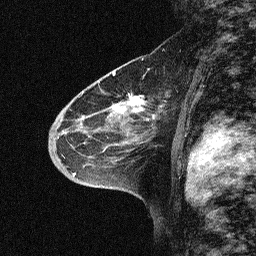
Breast MRI (dynamic contrast-enhanced), one sagittal slice. Slice 39 of 64 in the series (ordered by position). Dynamic contrast-enhanced study with each time point stored as its own series, time point 2 of 3 at this slice position (early post-contrast, ordered by acquisition time). 1.5 T. TE 4.5 ms, TR 11 ms. 2.06 mm slice thickness. 256 × 256 image matrix. Female patient, age 46 years. Case-level facts recorded for this patient, not image findings: setting: breast cancer imaged before/during neoadjuvant chemotherapy; receptor status: HER2-positive.
Structures marked on this image (semi-automatically segmented with operator editing):
- analysis volume of interest (the breast-tissue region the enhancement analysis was run in; not a lesion): bounding box <46,51,180,169> (left, top, right, bottom; pixels)
- tumour enhancement mask (voxels above the 90 % enhancement threshold inside the analysis volume of interest): <115,95,145,112>